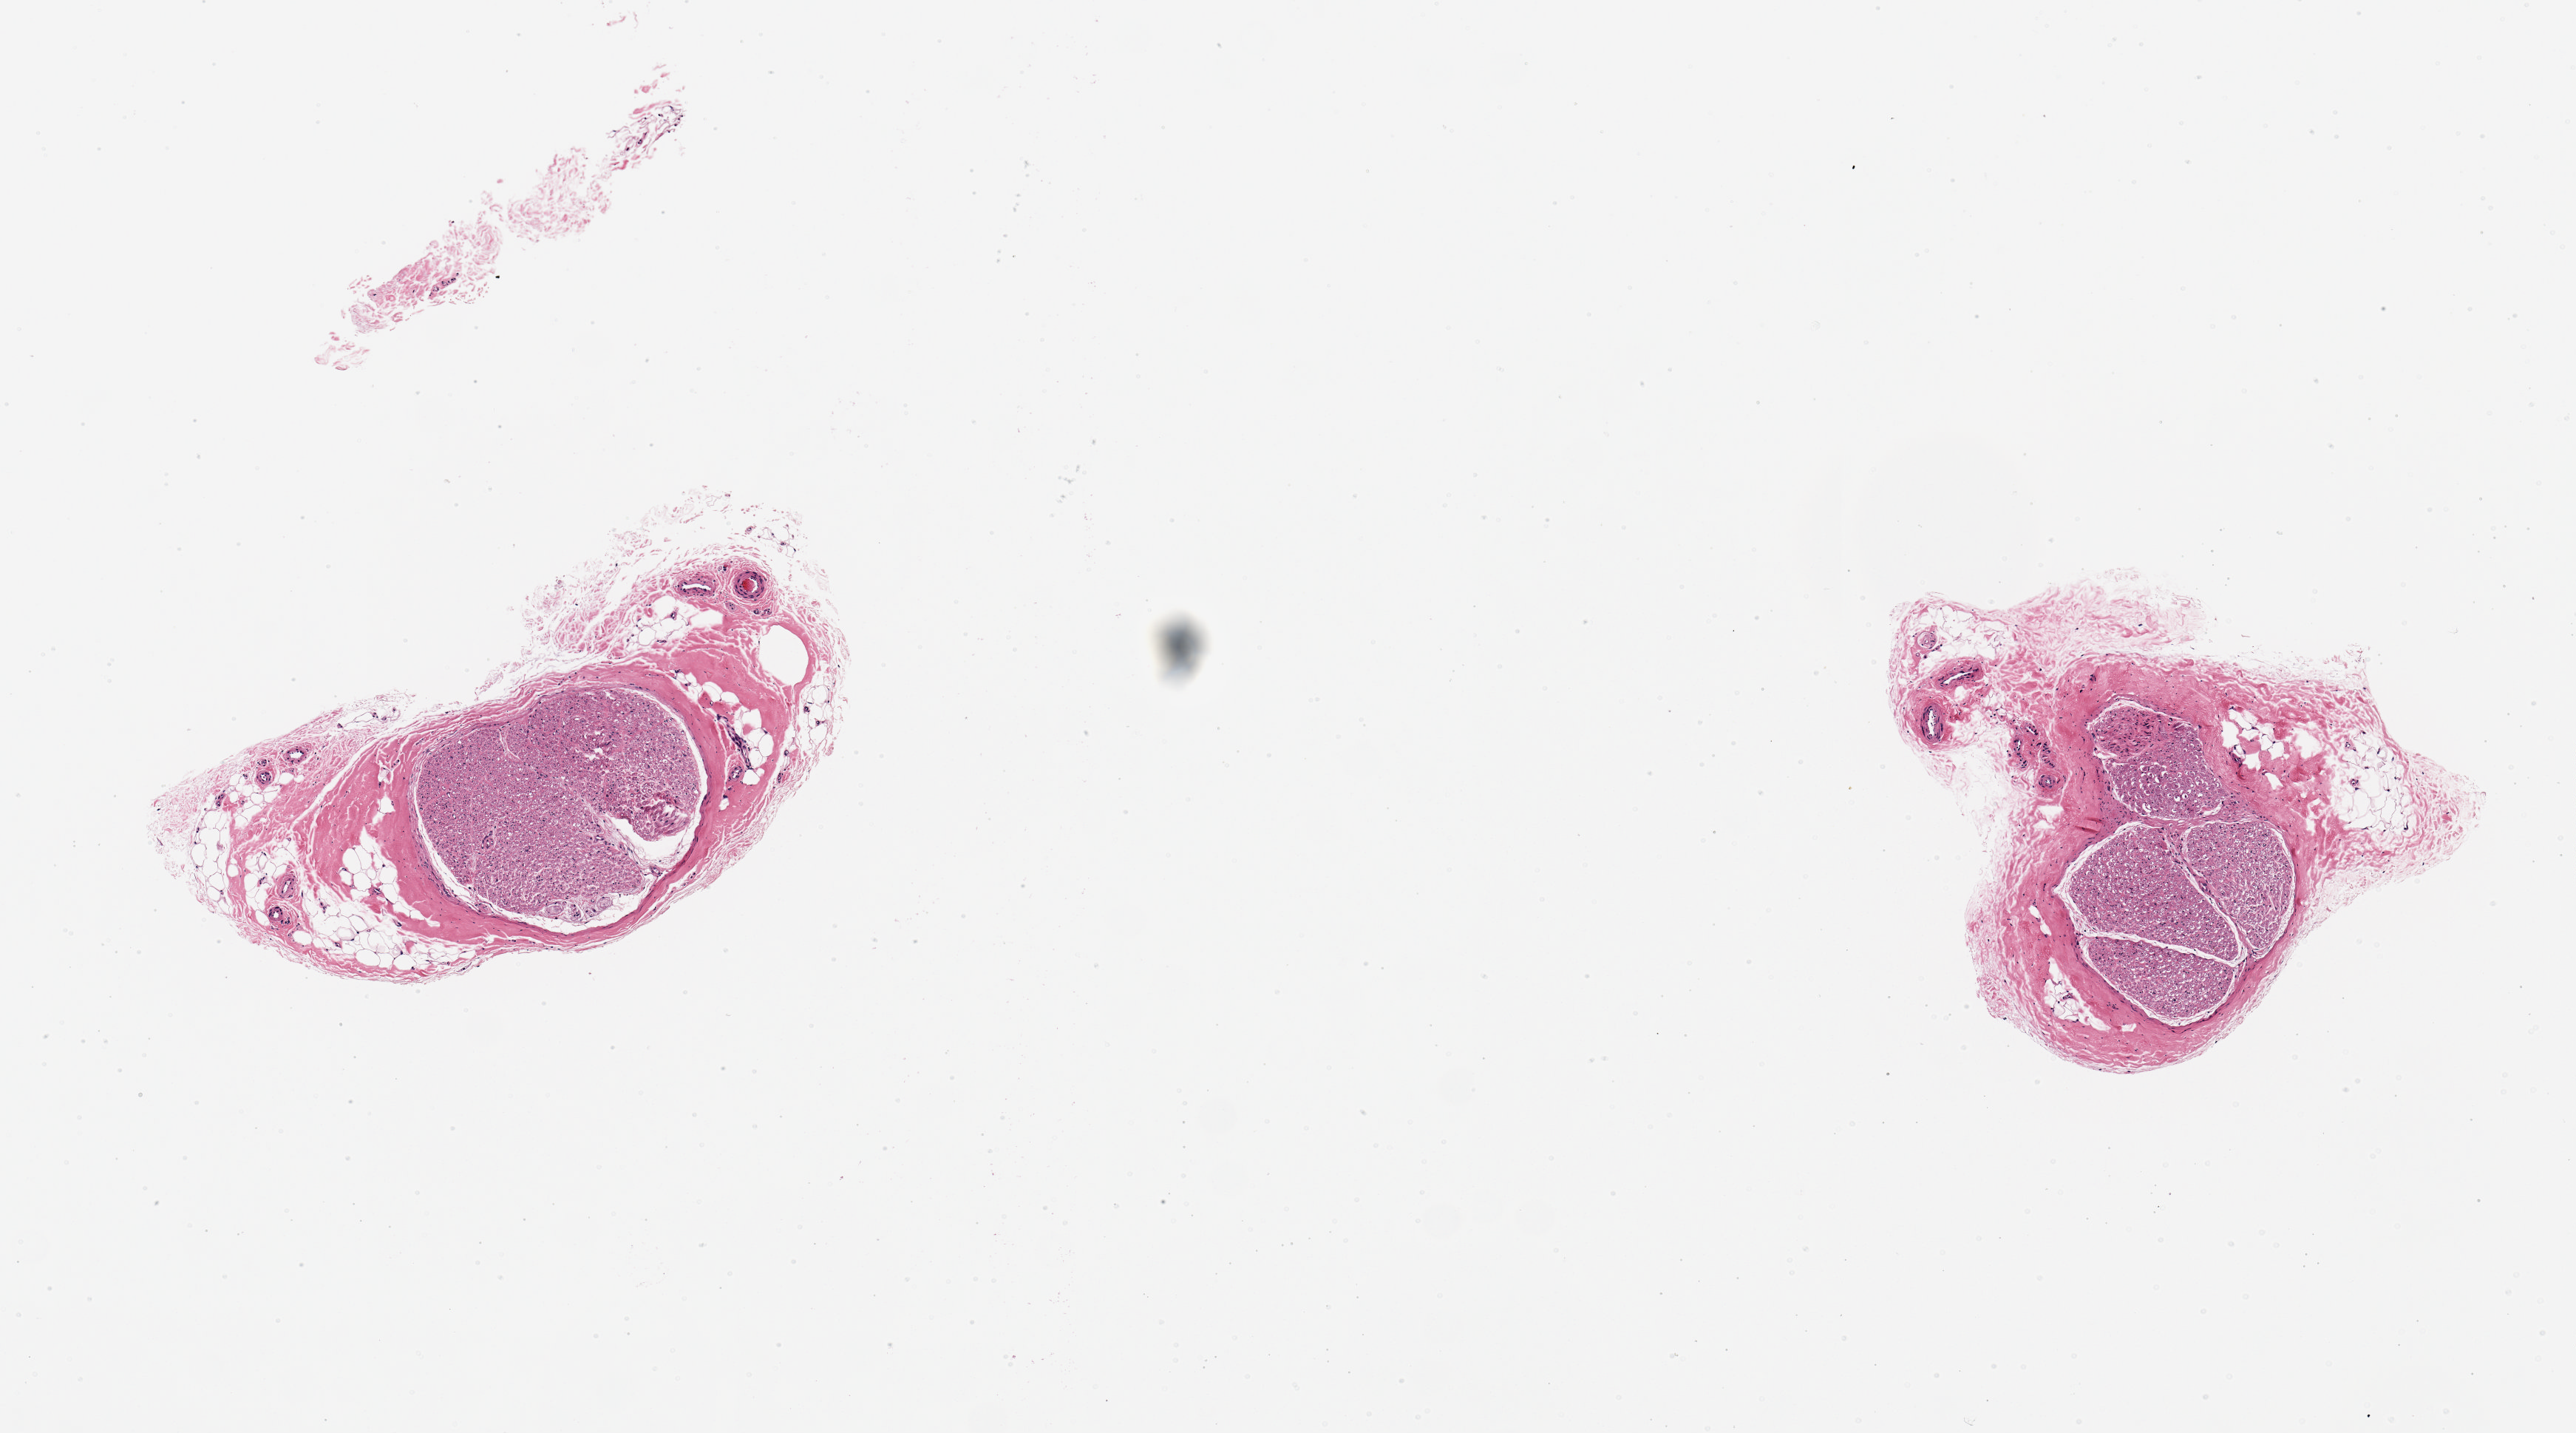
Whole-slide image, hematoxylin and eosin (H&E) stain — low-resolution overview of the scanned area, about 6.9 x 3.8 mm, PAXgene-fixed paraffin-embedded (PFPE) section, section of tibial nerve (target tissue), donor tissue sample. Donor: female.
• reviewer comment on this tissue sample: 2 pieces; 40% of aliquot is fat and stroma; nerve is ~1.2mm